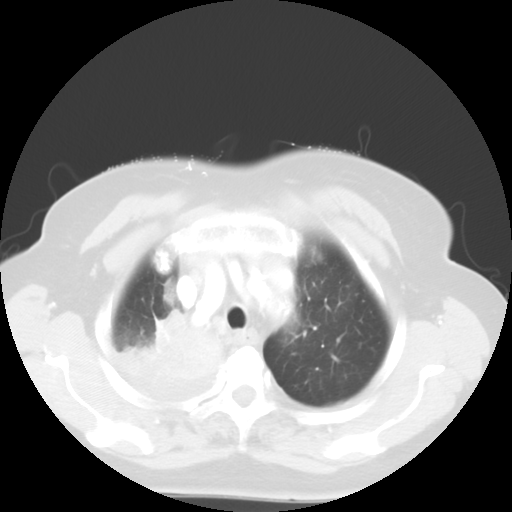
Chest CT, one axial slice; slice 44 of 52 in the series (ordered by position); reconstruction kernel STANDARD; 120 kVp; lung window (W 1500 / L -600 HU); 5 mm slice thickness; 512 × 512 image matrix, field of view 333 × 333 mm. Patient: female, 81 years. Case-level facts recorded for this patient, not image findings: clinical TNM (as recorded): T4 N3 M1b.
Annotated regions visible in this slice (bounding box drawn by a radiologist):
- lung tumour (recorded histology: adenocarcinoma): box from (x=115, y=309) to (x=227, y=389) px